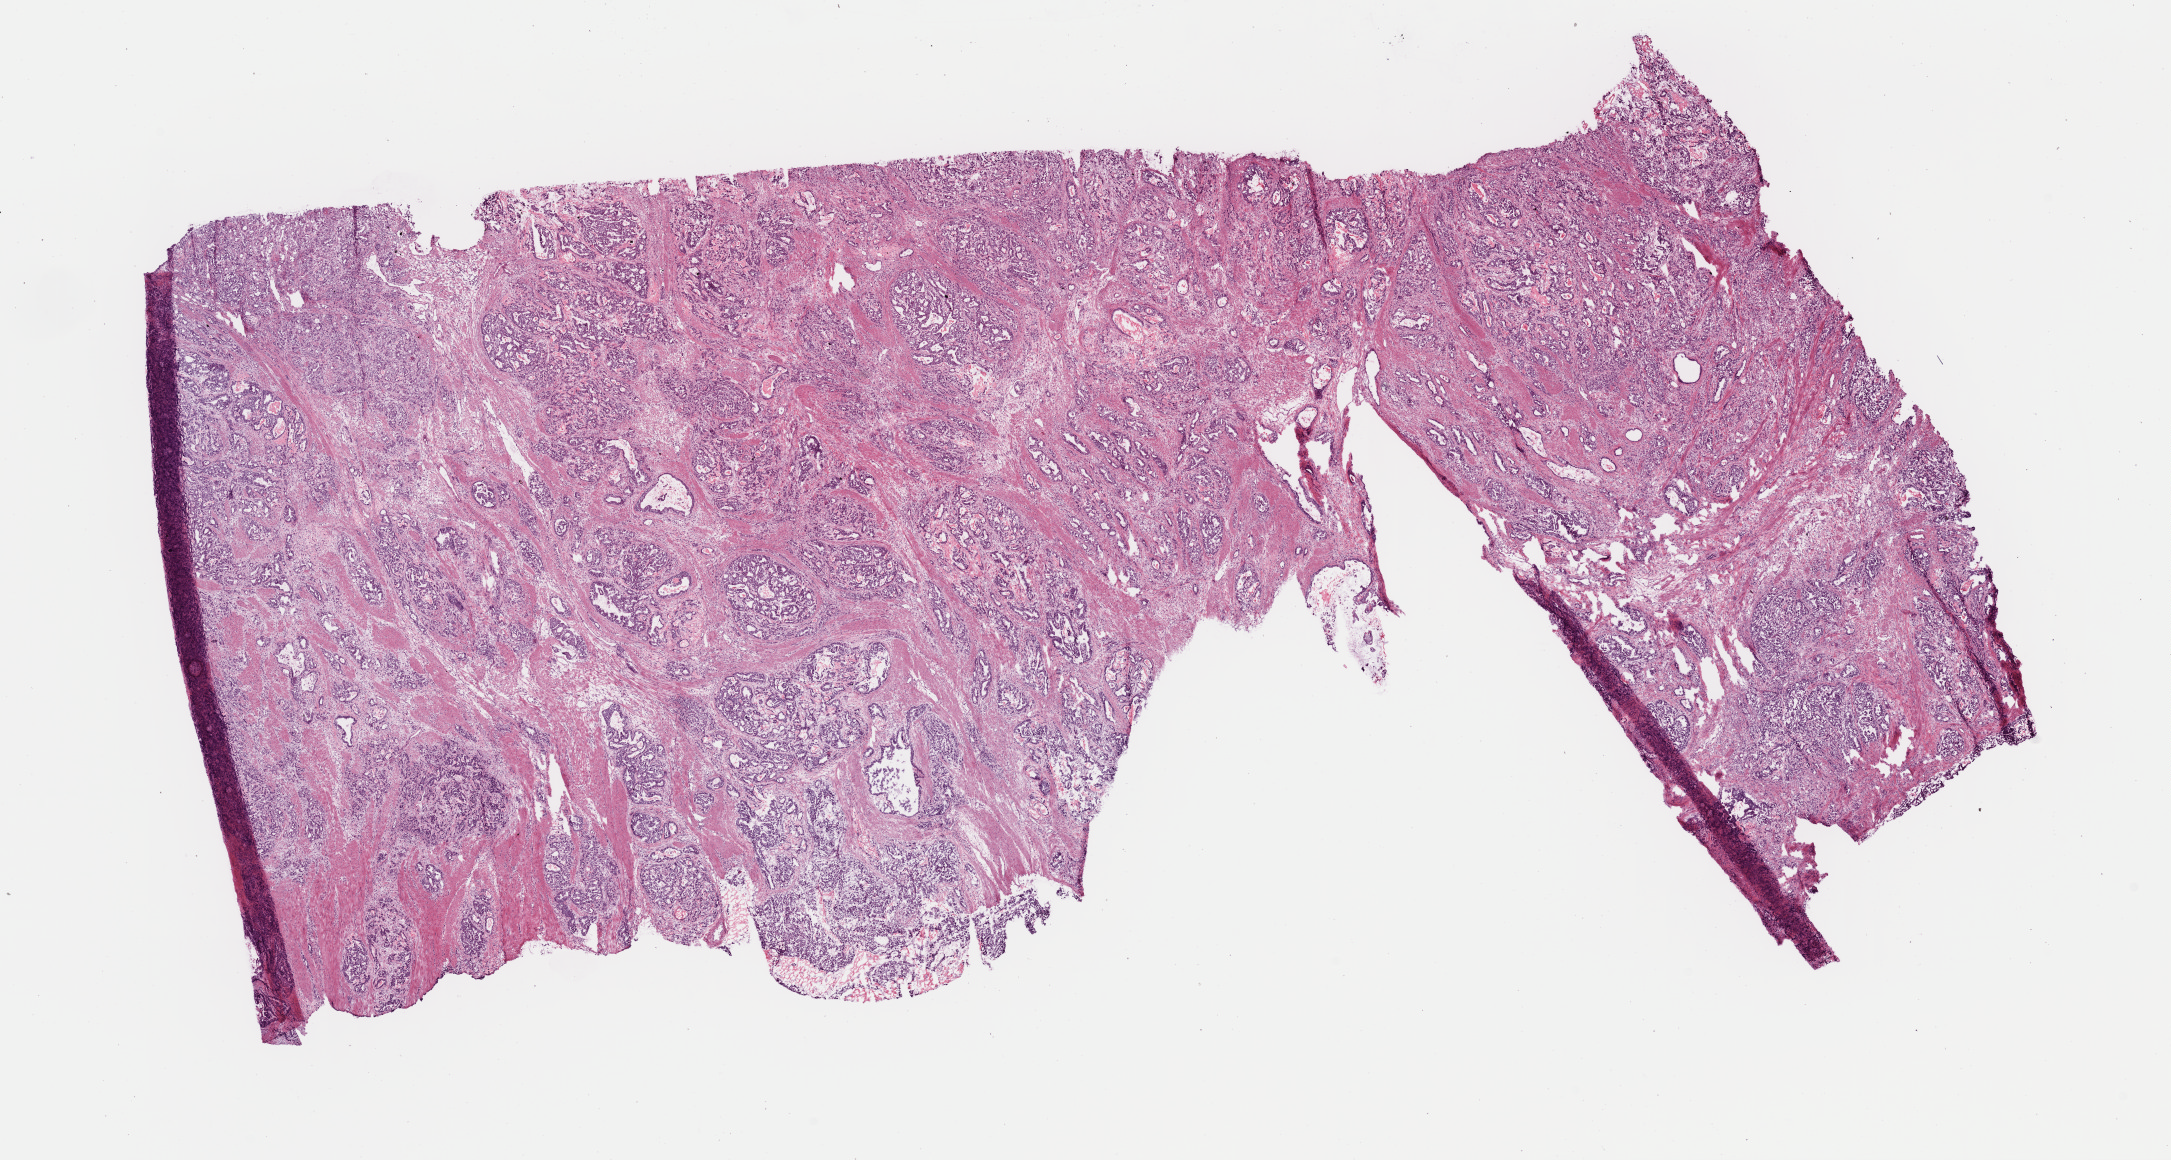
Digitized Hematoxylin and eosin (H&E) stained tissue section (whole slide) — low-resolution overview of the scanned area, about 17.2 x 9.2 mm (acquisition: 40x scan). Frozen section from the bottom of the tissue portion. Stomach, primary tumour sample. Female, age 86 years at initial diagnosis. Histologic grade: G2 (moderately differentiated). Composition of this section per pathologist review: tumour cells 70%, tumour nuclei 85%, normal cells 0%, stromal cells 20%, necrosis 10%.
AJCC pathologic stage: IV (7th edition). TNM: T4 N3 M1. Diagnosis: Adenocarcinoma, NOS (gastric antrum).